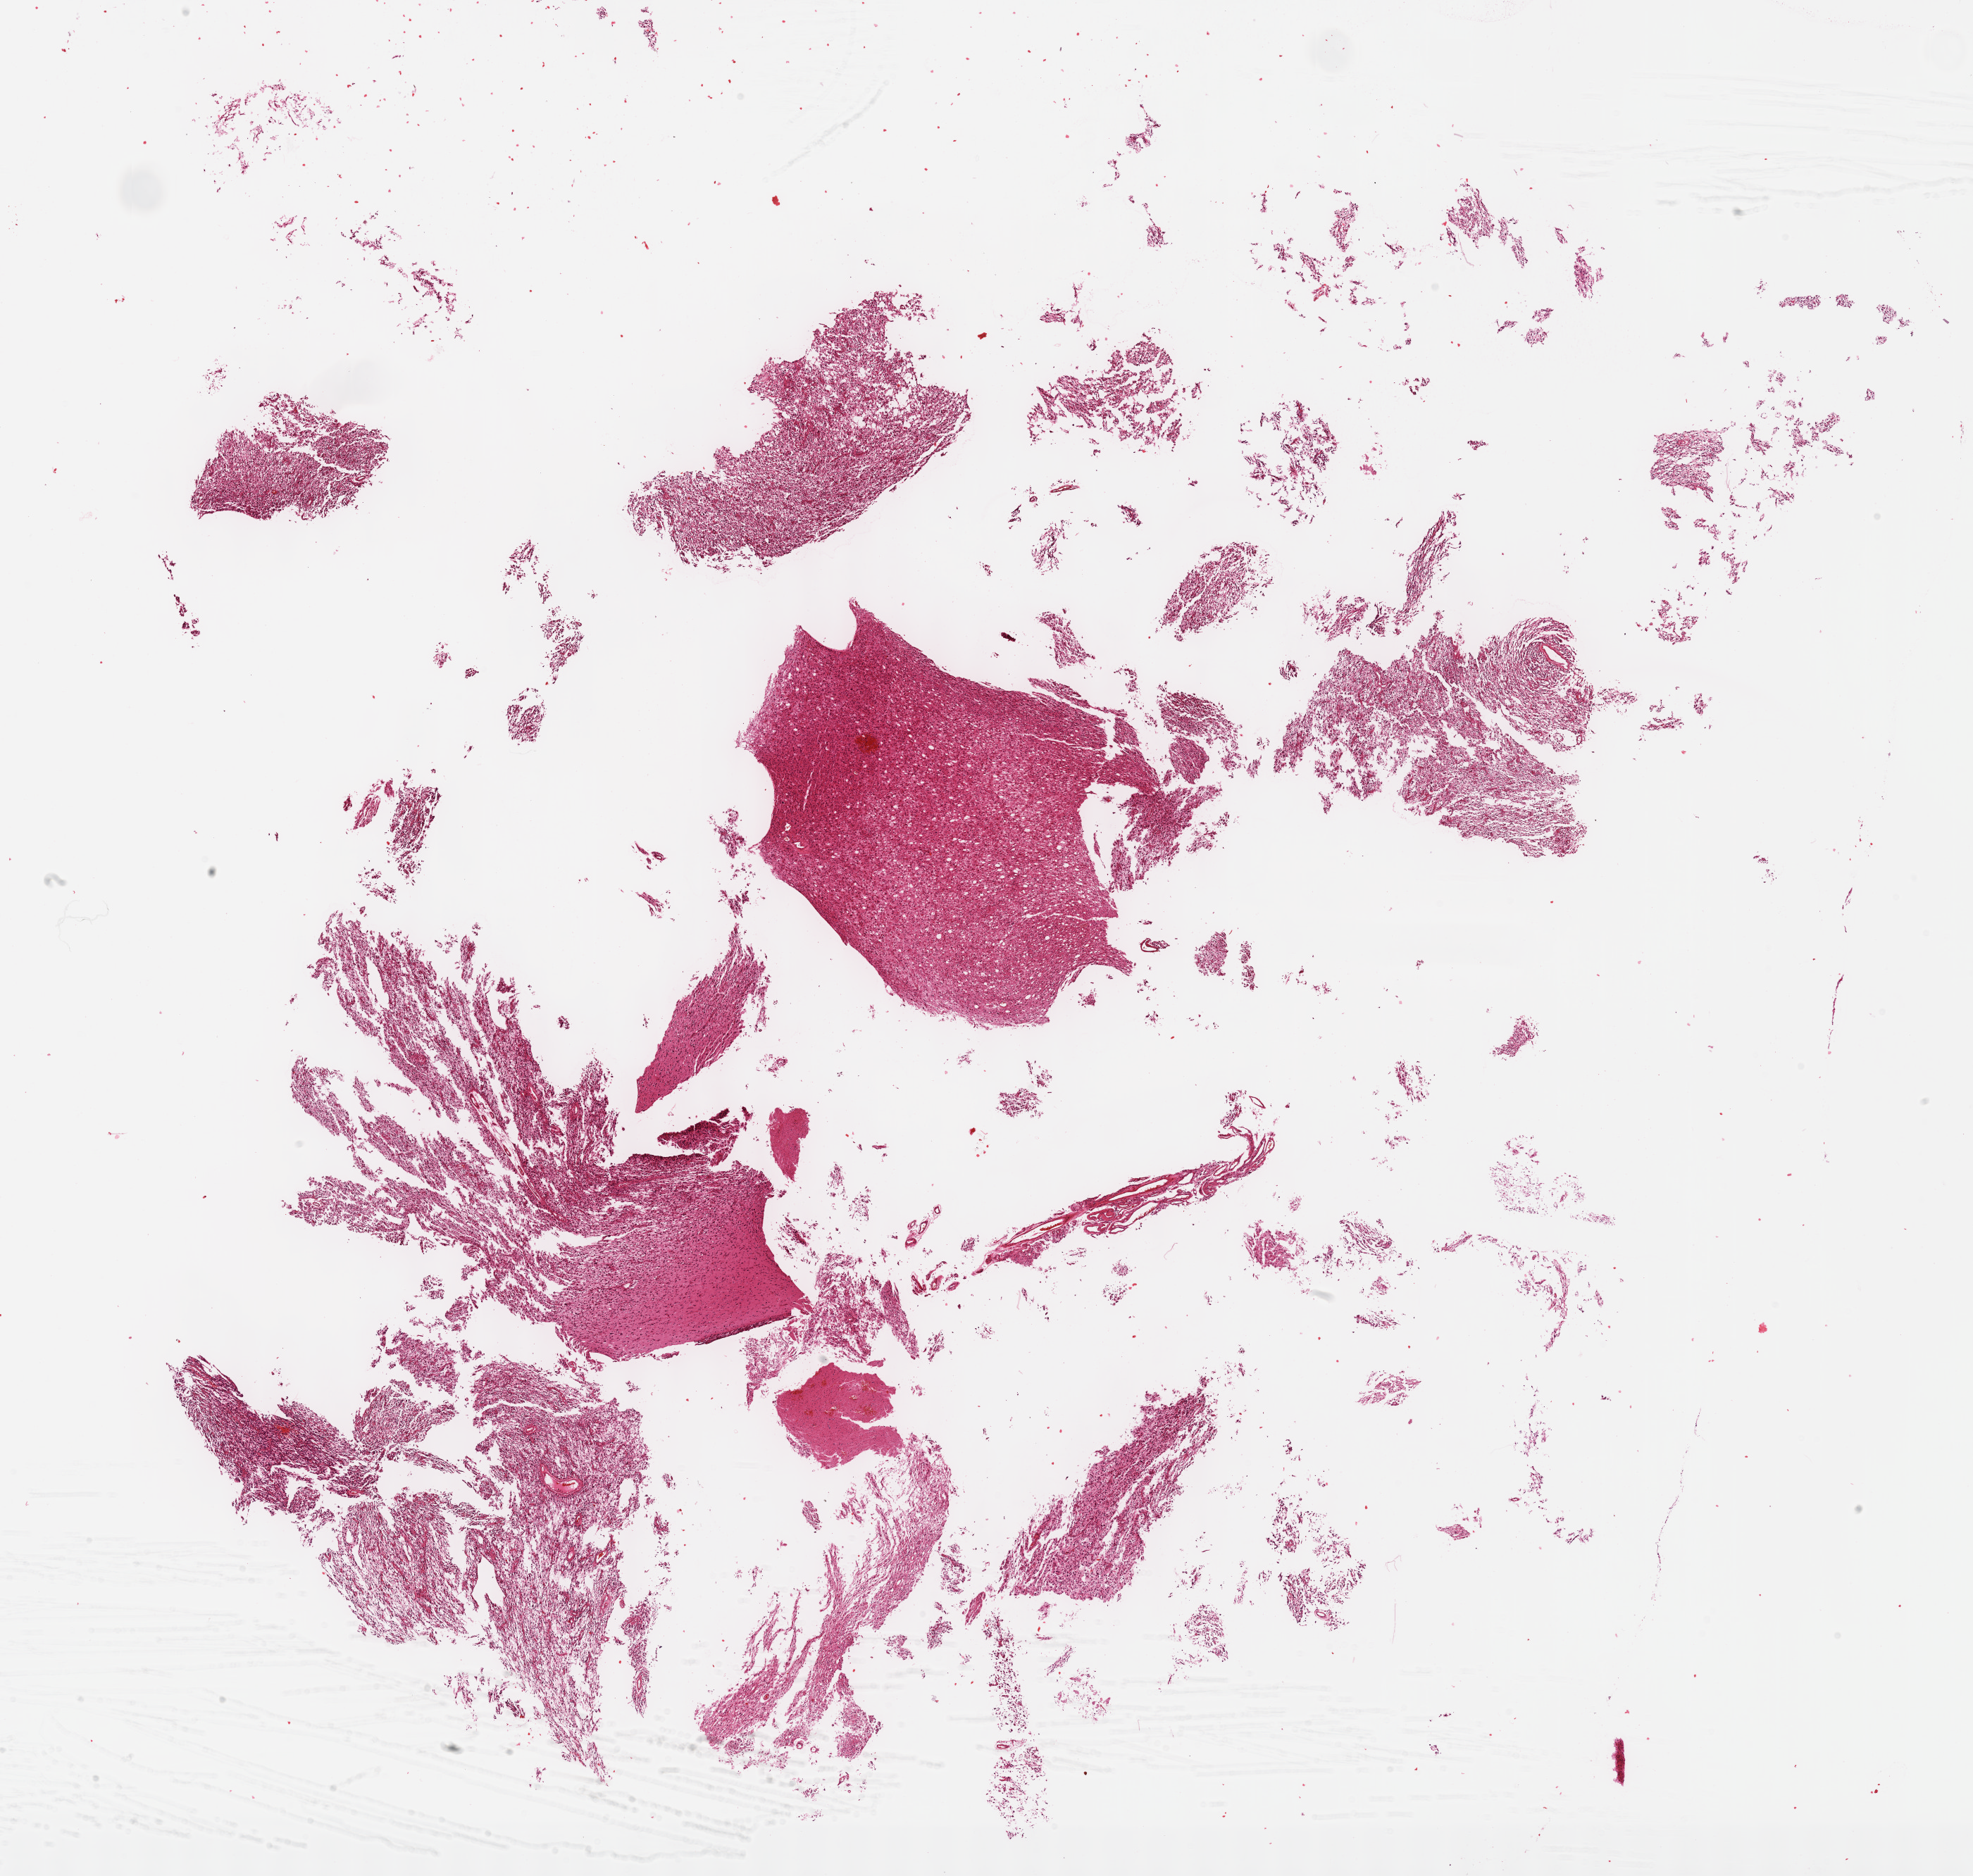
Whole-slide histology image, H&E-stained, low-resolution overview of the scanned area, about 22.7 x 21.5 mm, FFPE section, primary tumour sample from the brain. Patient: female, age at initial diagnosis 48 years. Histologic grade: G3 (poorly differentiated).
Laterality: right. Pathologic diagnosis: Astrocytoma, anaplastic.